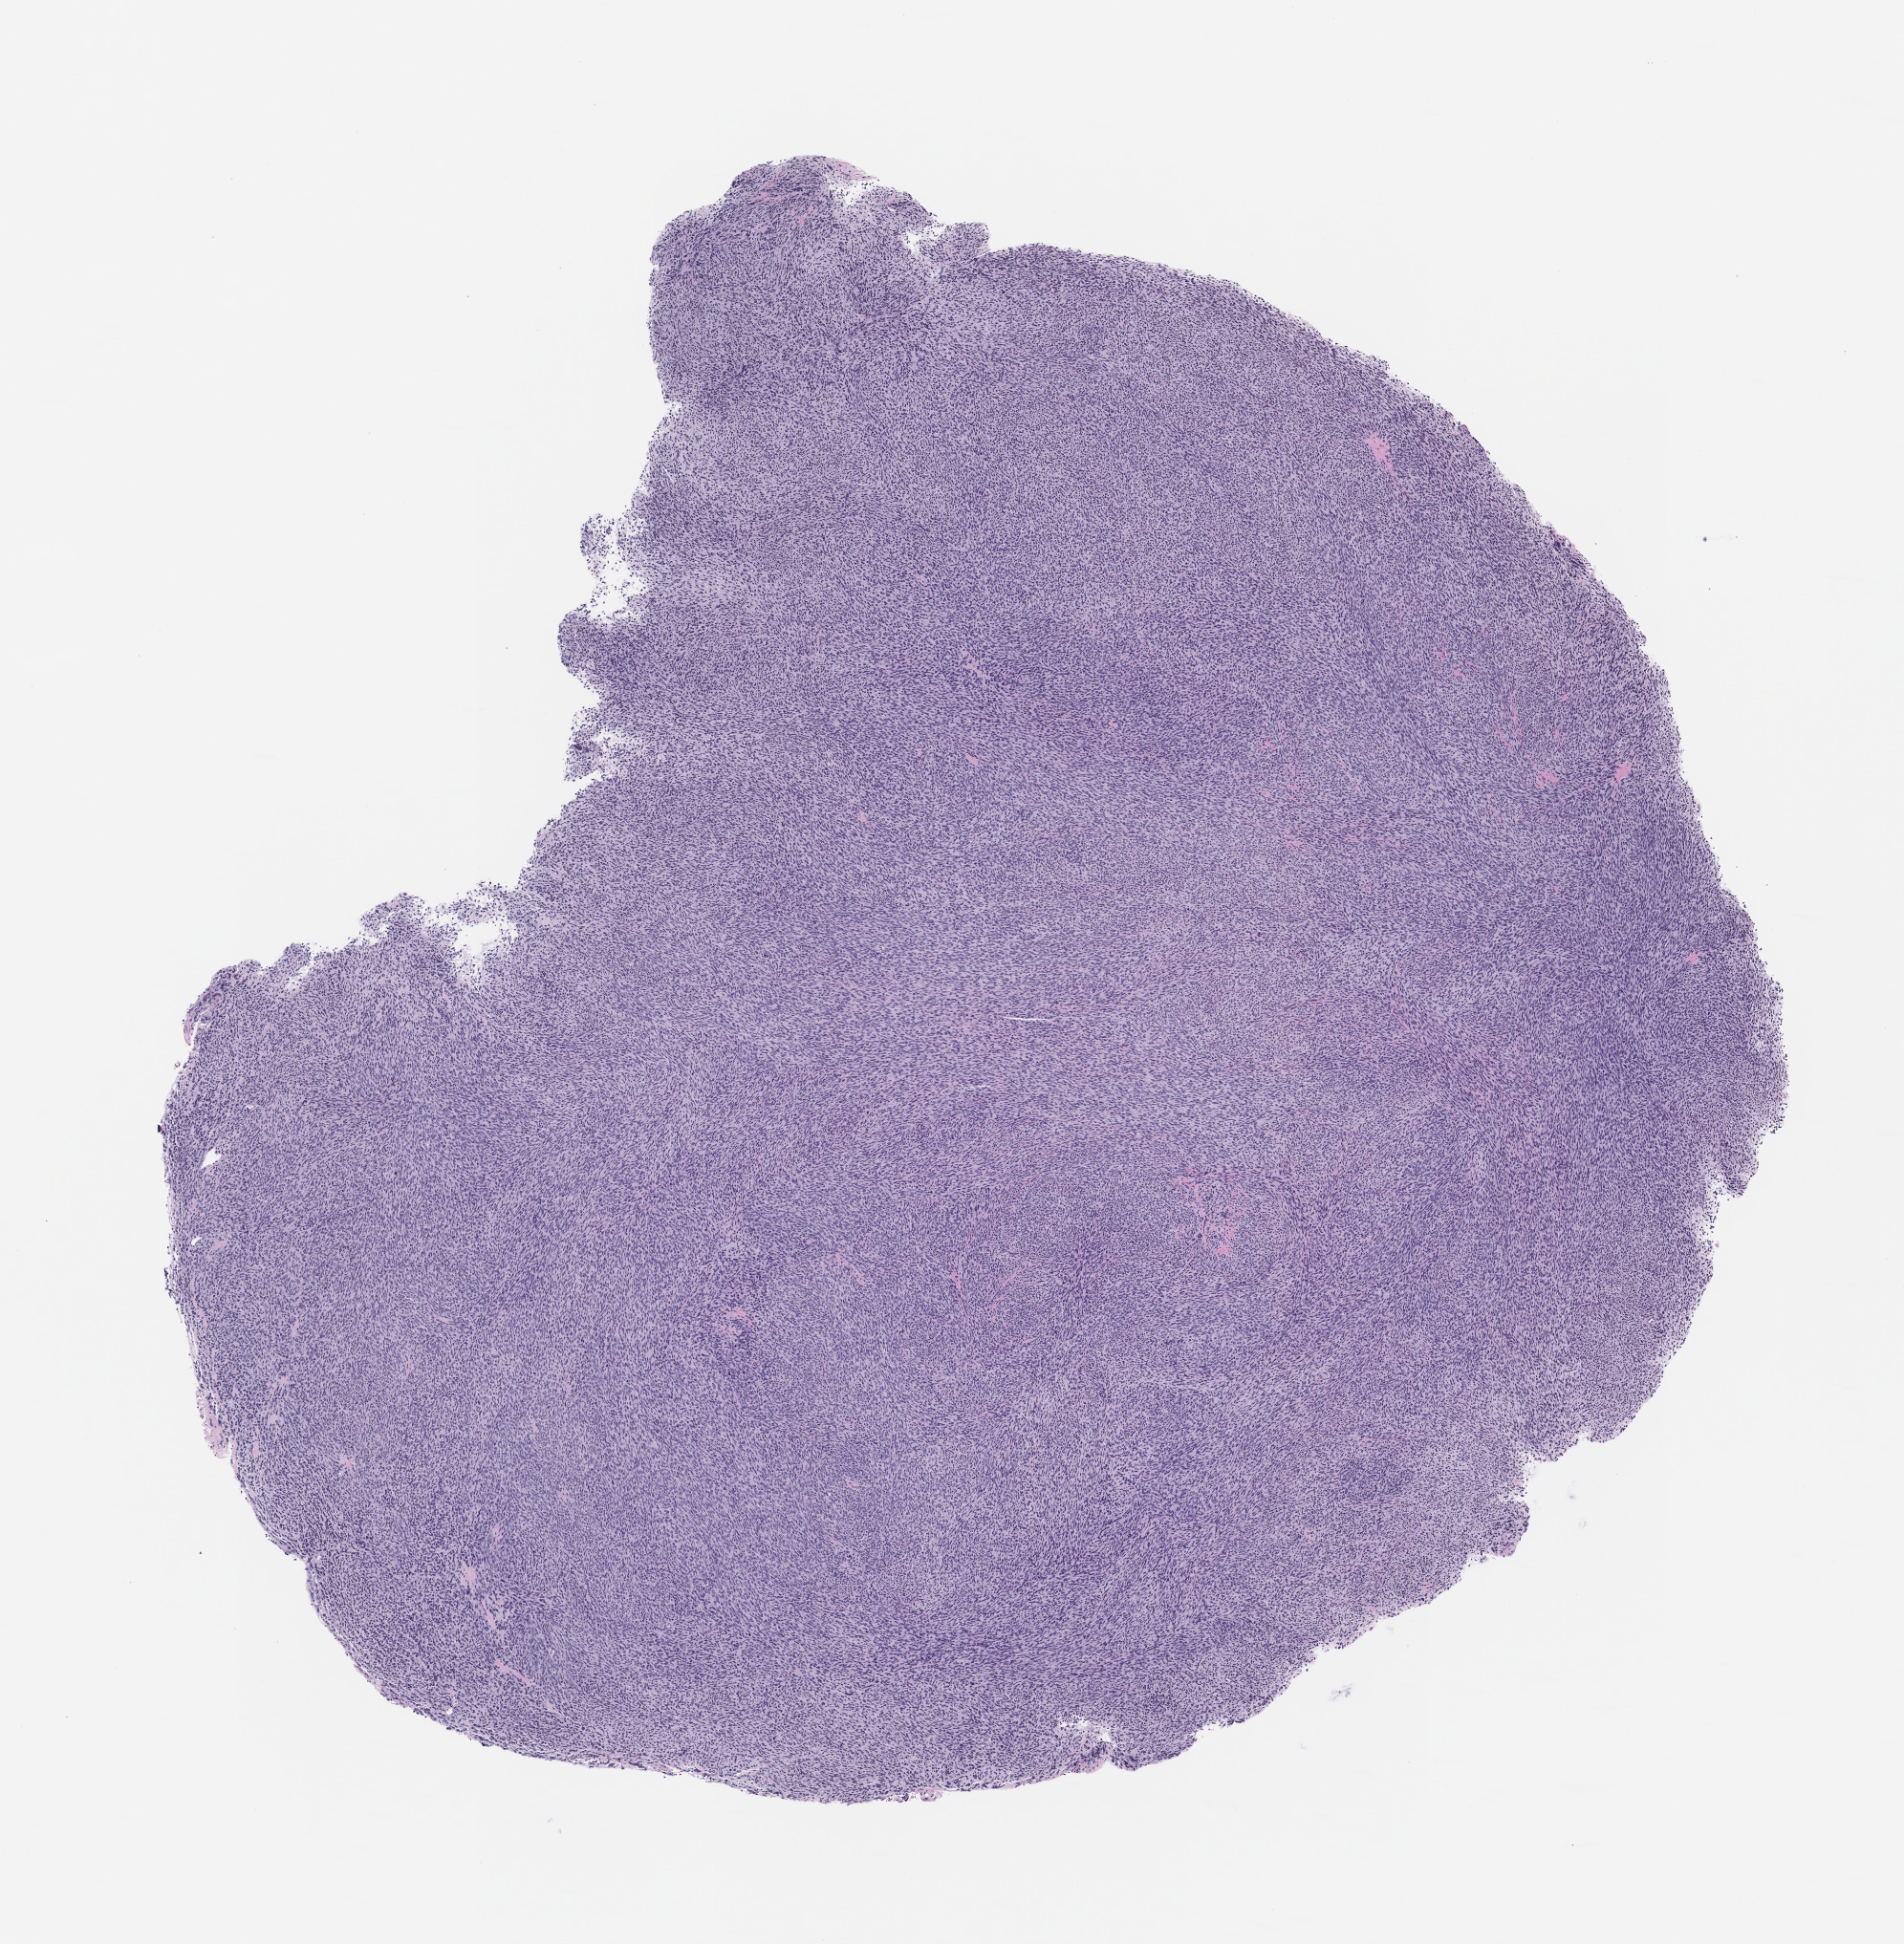
Haematoxylin and eosin whole-slide image of a patient-derived xenograft (PDX) tumor grown in a mouse, passage 2, low-resolution overview of the scanned area, about 8.0 x 8.2 mm. Formalin-fixed, paraffin-embedded (FFPE) tissue. Originating tumor site category: peripheral nervous system.
• originating patient diagnosis: Malignant Peripheral Nerve Sheath Tumor